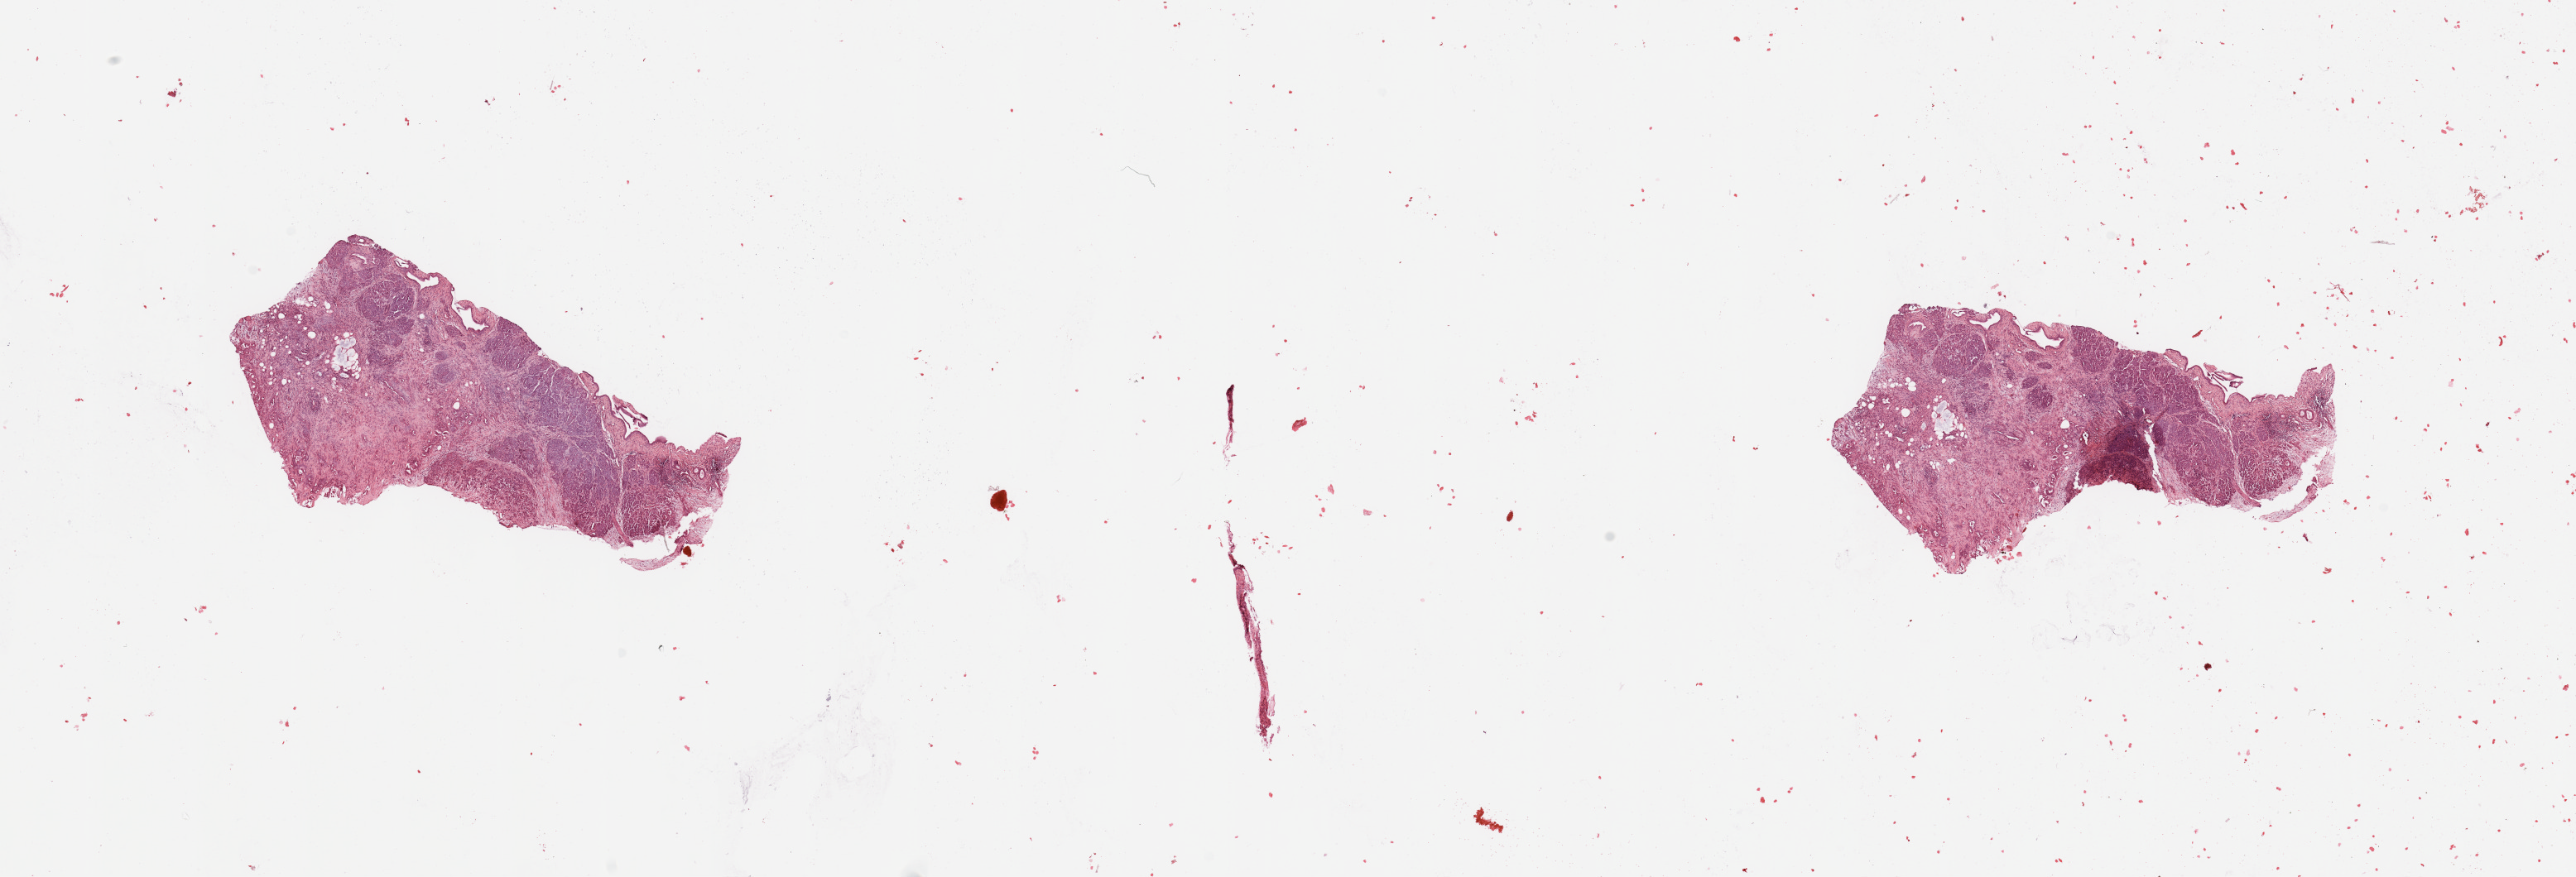
Whole-slide histology image, H&E-stained, low-resolution overview of the scanned area, about 24.6 x 8.4 mm; tumour tissue sample, sampled site: pancreas. Patient: female, age 69 years. Histologic grade: G2 (moderately differentiated). Composition of this section per pathologist review: tumour nuclei 10%, necrosis 0%.
* AJCC pathologic stage: IIB
* primary tumour site (as recorded): head
* diagnosis: Infiltrating duct carcinoma, NOS